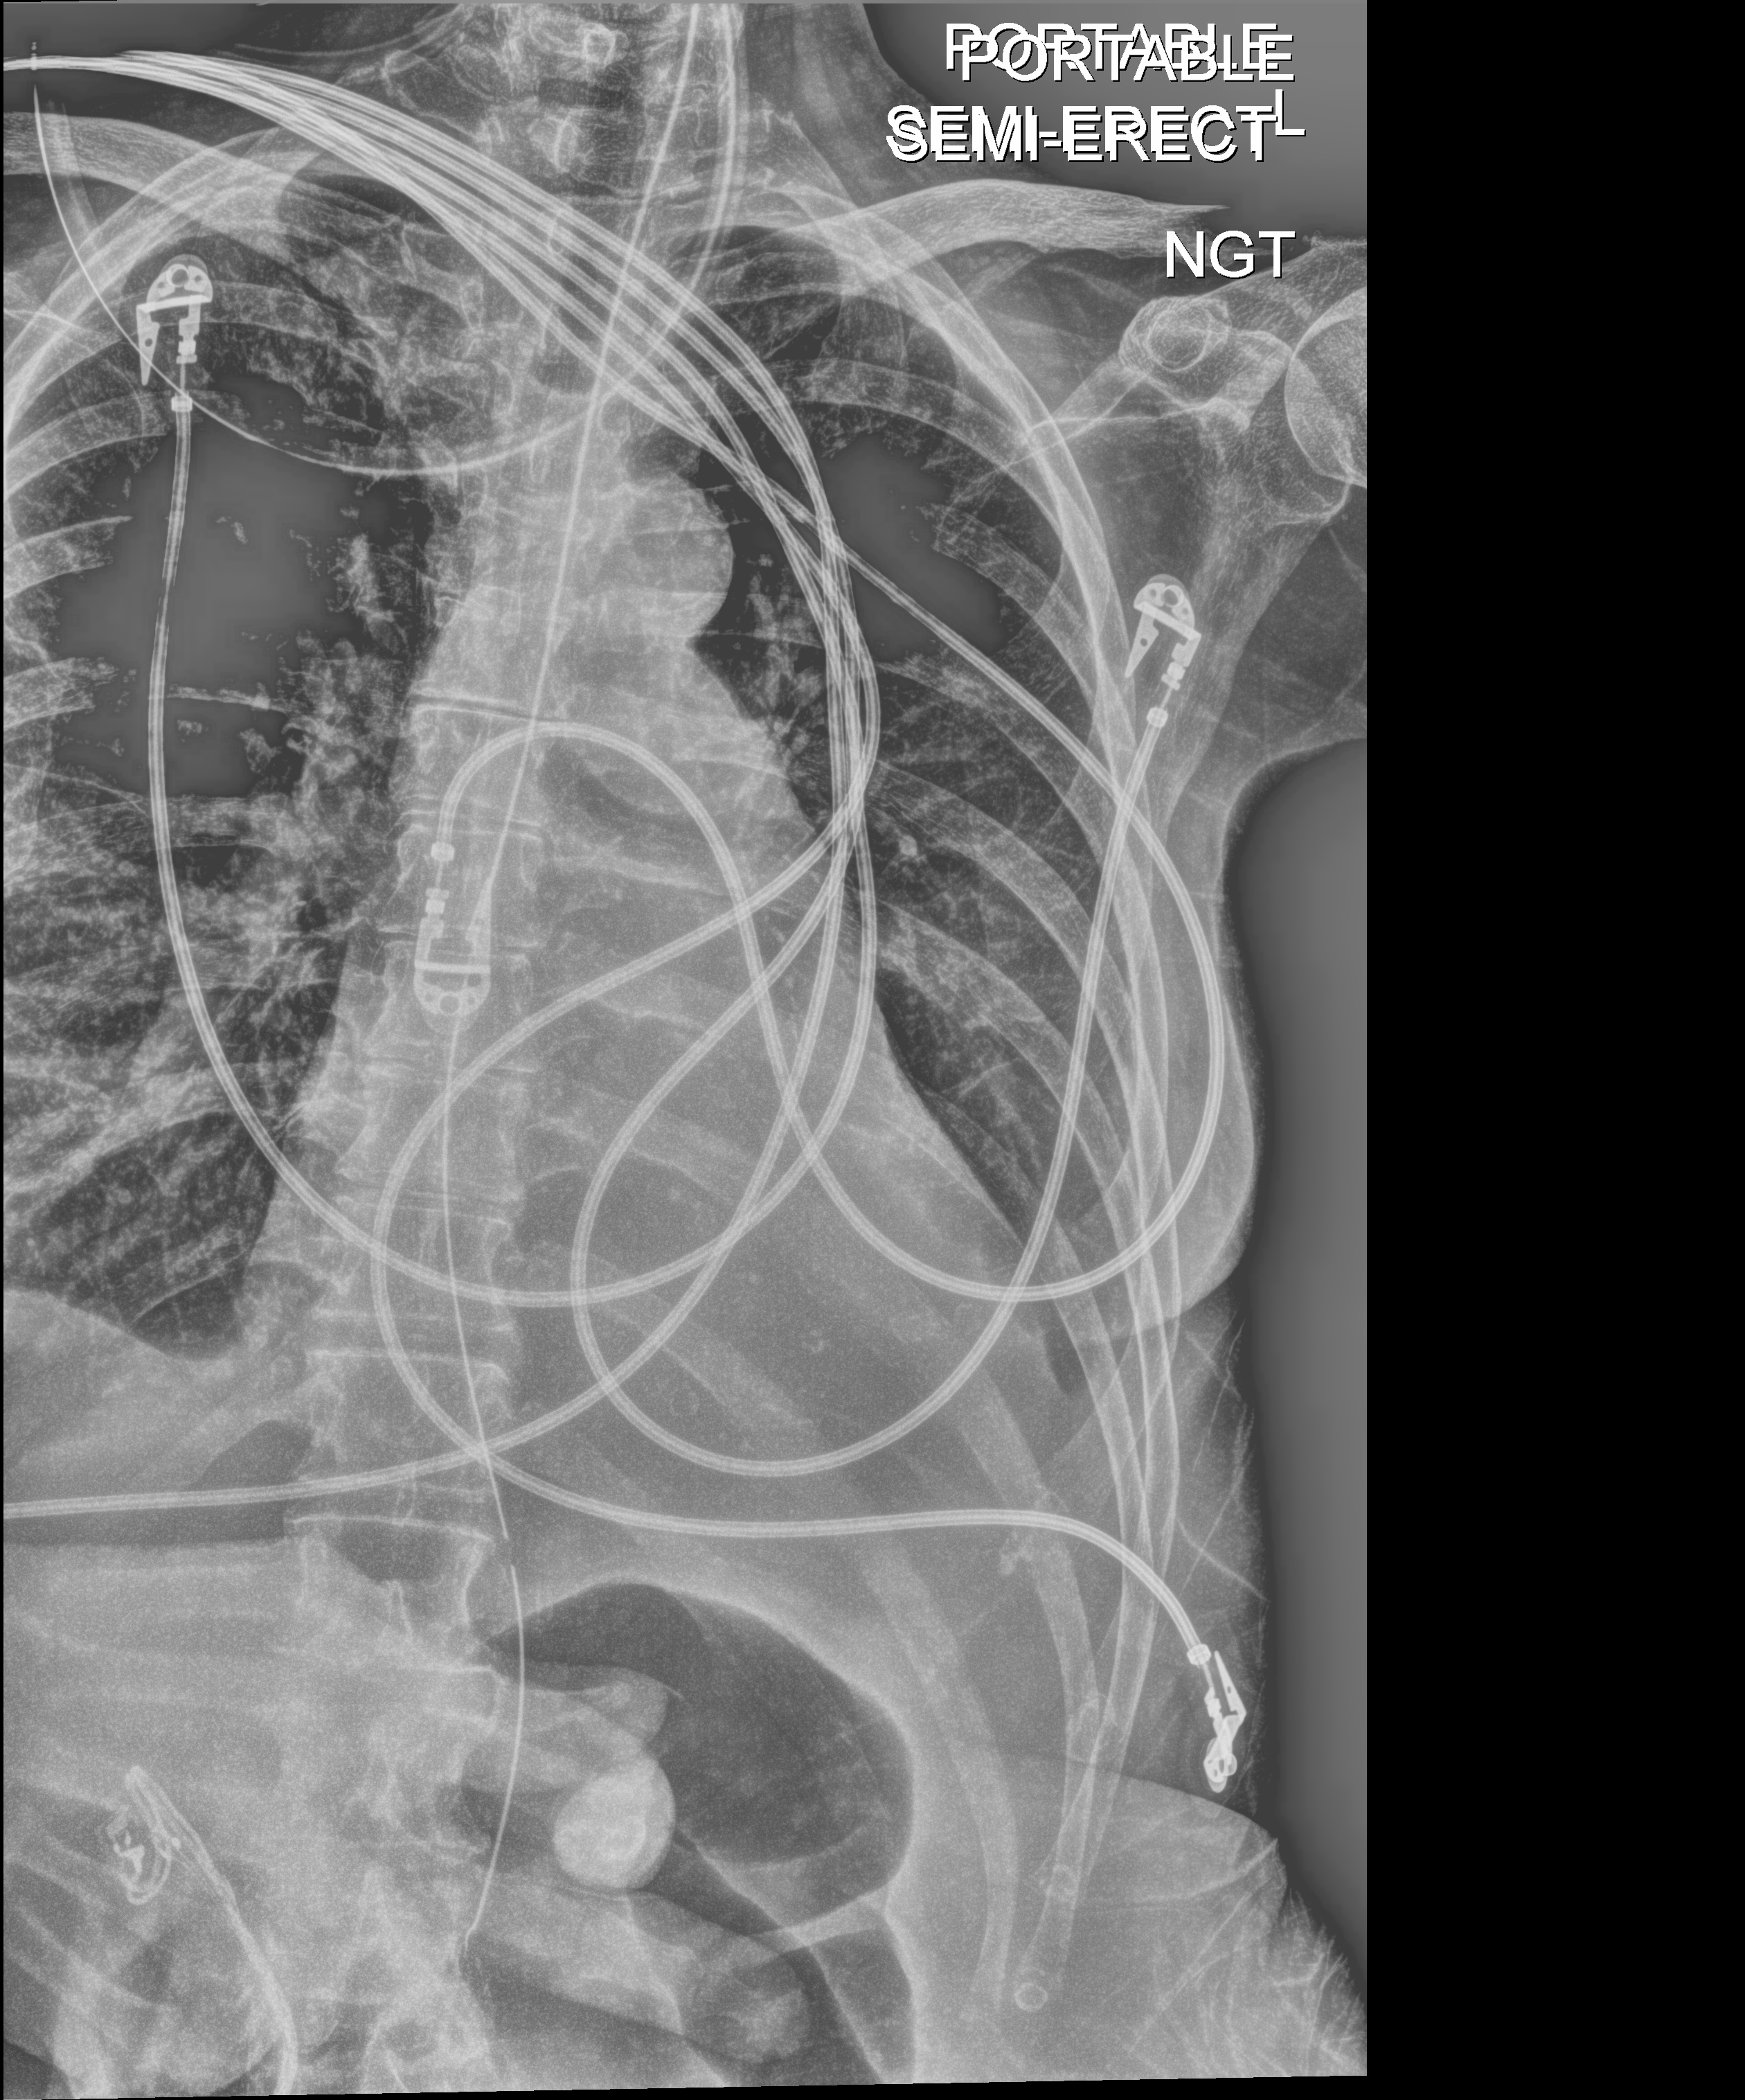
Bedside chest radiograph (digital radiography), anteroposterior (AP) projection. Patient hospitalised with COVID-19; female, aged 60–74 years.
From the hospital-stay record, not from the radiograph (when in the stay this image was taken is not recorded): admitted to intensive care during this hospital stay: yes; length of hospital stay: 38 days.